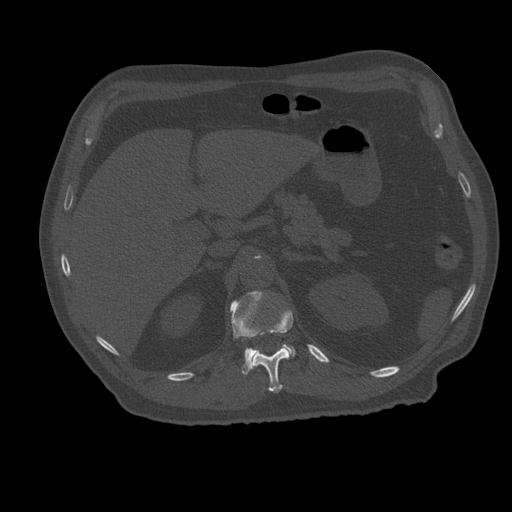
CT including the spine, one axial slice. Position 253 of 399 along the scan axis. Reconstruction kernel STANDARD. 120 kVp. Bone window (W 1800 / L 400 HU). 512 × 512 image matrix. Patient age 73 years. Case-level facts recorded for this patient, not image findings: primary cancer: prostate; vertebrae with lytic lesions (as recorded): L2.
Outlined on this slice (semi-automatically segmented with operator editing):
- L1 vertebra: bounding box (x1, y1, x2, y2) in pixels: (230, 291, 296, 375)
- T12 vertebra: (252, 310, 294, 393)